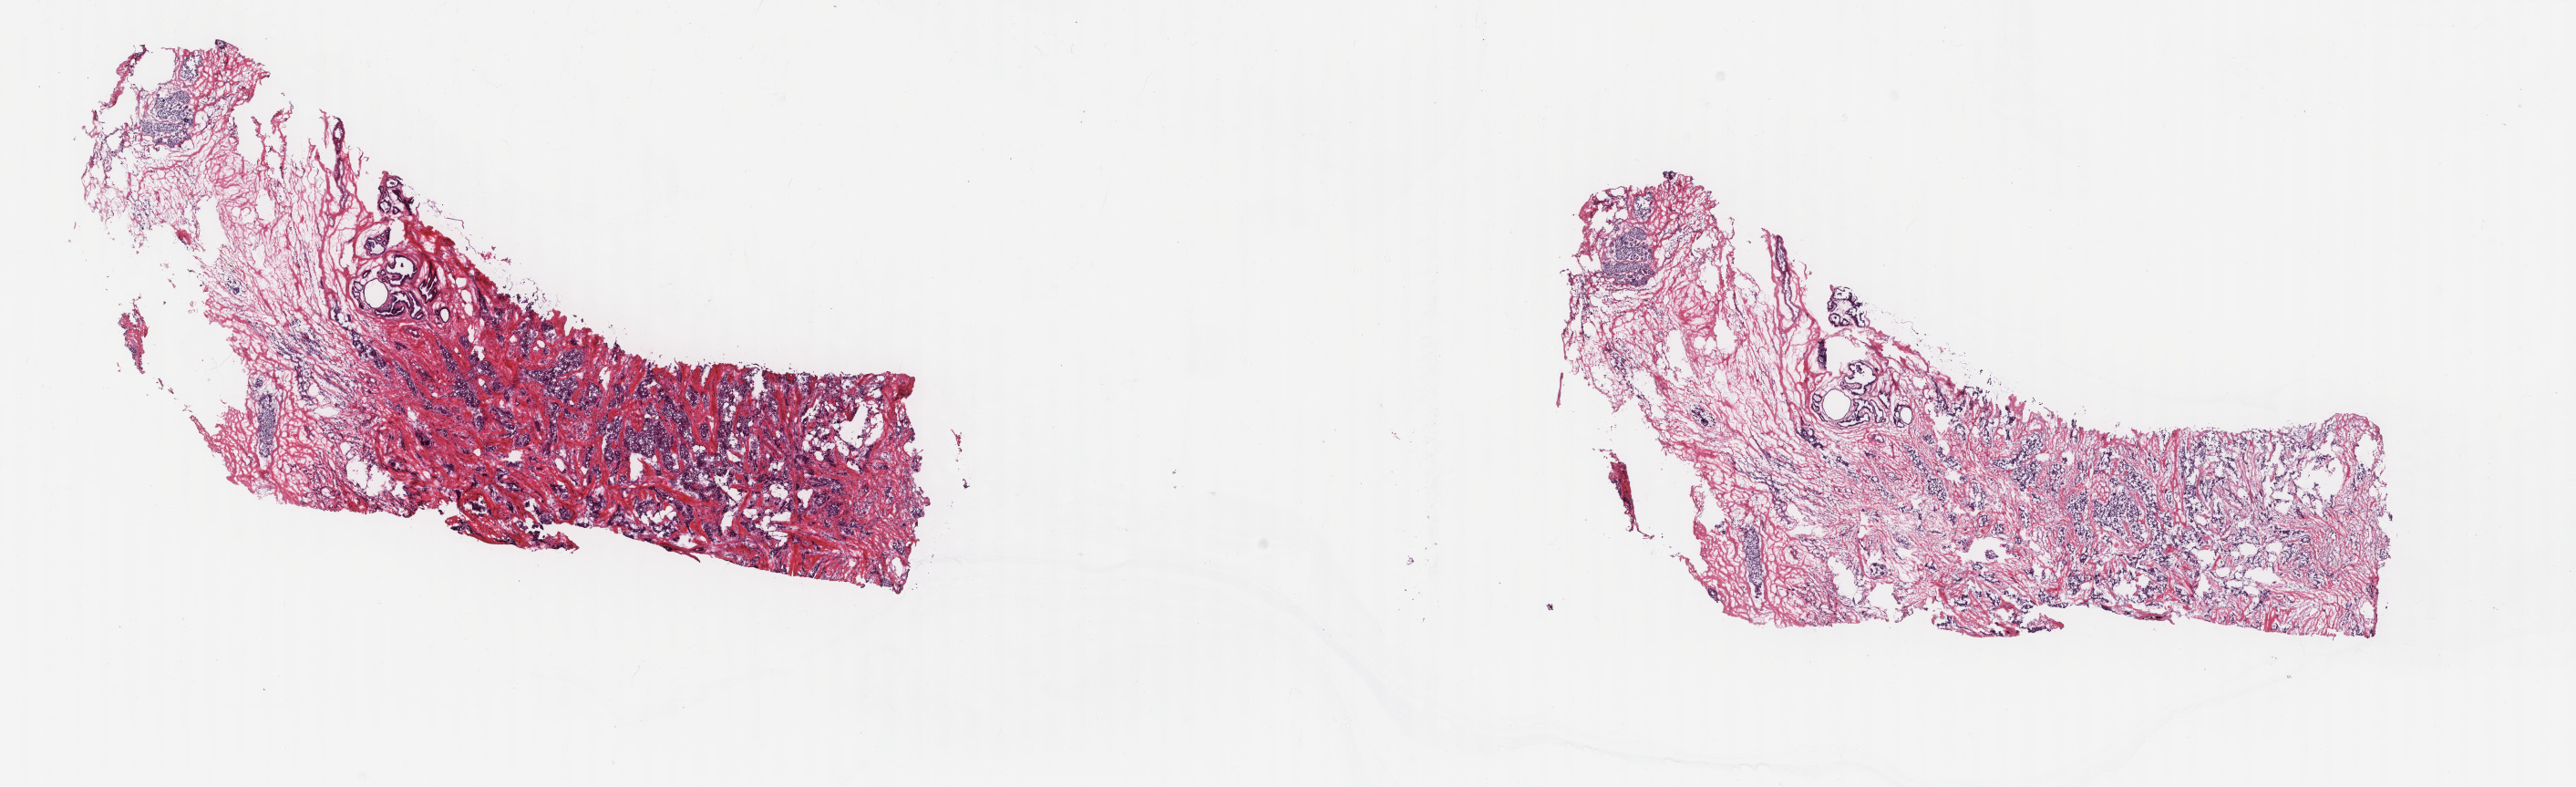
Digitized H&E tissue section (whole slide) — a low-resolution overview of the entire scanned area, about 22.4 x 6.8 mm (acquisition: 40x scan); frozen section from the top of the tissue portion; breast, primary tumour sample. Female patient; age at initial diagnosis 75 years. Slide review estimates, as recorded: tumour cells 30%, tumour nuclei 70%, normal cells 8%, stromal cells 61%, necrosis 1%. Inflammatory infiltration, as recorded: lymphocyte infiltration 2%, monocyte infiltration 1%, neutrophil infiltration 0%.
TNM: T3 N0 MX. Lymph nodes positive (case pathology): 0 of 2 examined. Laterality: right. AJCC pathologic stage: IIB (7th edition). Histologic diagnosis: Lobular carcinoma, NOS.